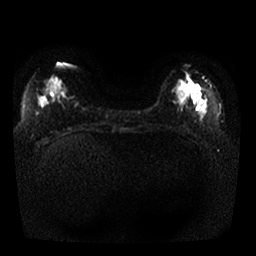
Breast MRI, one axial slice; position 9 of 25 along the scan axis; diffusion-weighted series; image 2 of 4 stored at this slice position (different b-values; order by instance number); 1.5 T; 4 mm slice thickness; 256 × 256 image matrix, field of view 330 × 330 mm. Female patient.
Structures marked on this image (manually delineated by an expert):
- tumour on diffusion-weighted imaging: bounding box <179,79,199,94> (left, top, right, bottom; pixels)